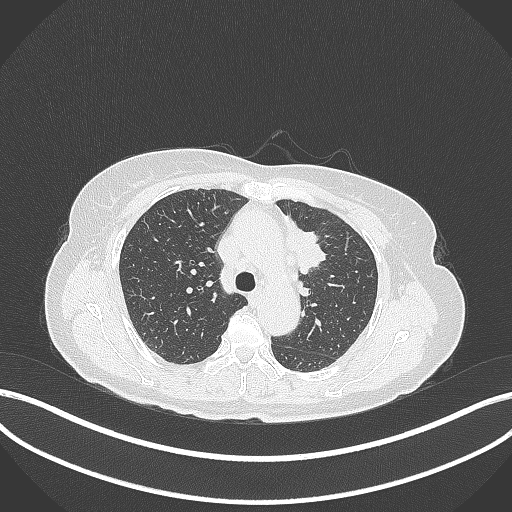
Chest CT, one axial slice; position 236 of 369 along the scan axis; reconstruction kernel B70f; 120 kVp; lung window (W 1500 / L -600 HU); 1 mm slice thickness; 512 × 512 image matrix, field of view 400 × 400 mm. Patient: female, 65 years. Case-level facts recorded for this patient, not image findings: clinical TNM (as recorded): T2a N0 M0; histopathological grade: G2-3.
Structures marked on this image (rectangle marked by the reading radiologist):
- lung tumour (recorded histology: adenocarcinoma): bounding box <283,215,329,275> (left, top, right, bottom; pixels)